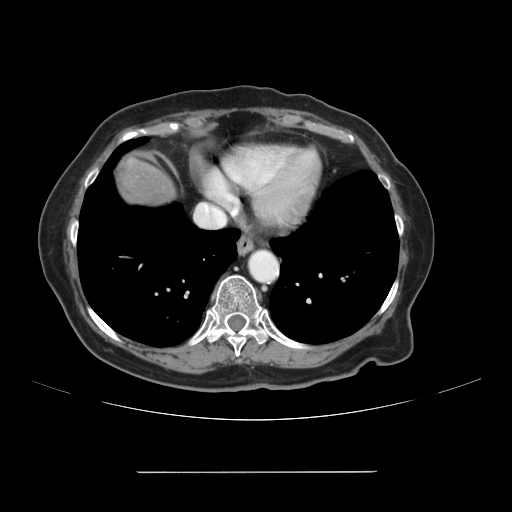
Contrast-enhanced abdominal CT, one axial slice; intravenous contrast given; soft-tissue window (W 400 / L 40 HU); 512 × 512 image matrix, field of view 400 × 400 mm. Female patient, age 74 years. From the clinical record (not read from this slice): diagnosis: colorectal cancer liver metastases, imaged before liver resection; multiple liver metastases: yes; largest metastasis: 1.1 cm.
Outlined on this slice (outlined manually by an expert reader):
- liver: bounding box (x1, y1, x2, y2) in pixels: (115, 155, 174, 208)